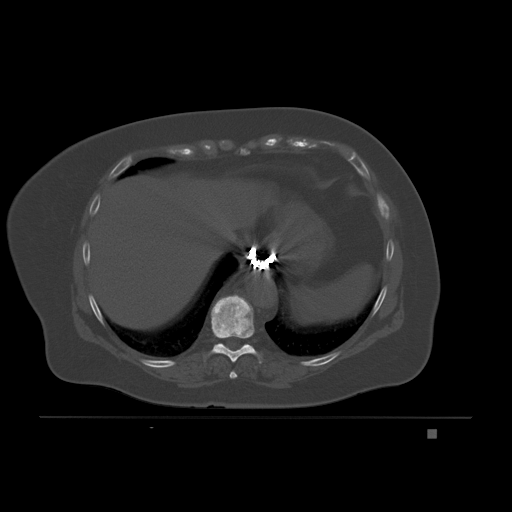
CT including the spine, one axial slice; position 108 of 221 along the scan axis; bone window (W 1800 / L 400 HU); 512 × 512 image matrix, field of view 474 × 474 mm. Patient: female, 63 years. From the clinical record (not read from this slice): primary cancer: breast.
Outlined on this slice (semi-automatic segmentation, software-assisted and operator-edited):
- T8 vertebra: bounding box <229,371,237,379> (left, top, right, bottom; pixels)
- T9 vertebra: <204,295,262,364>